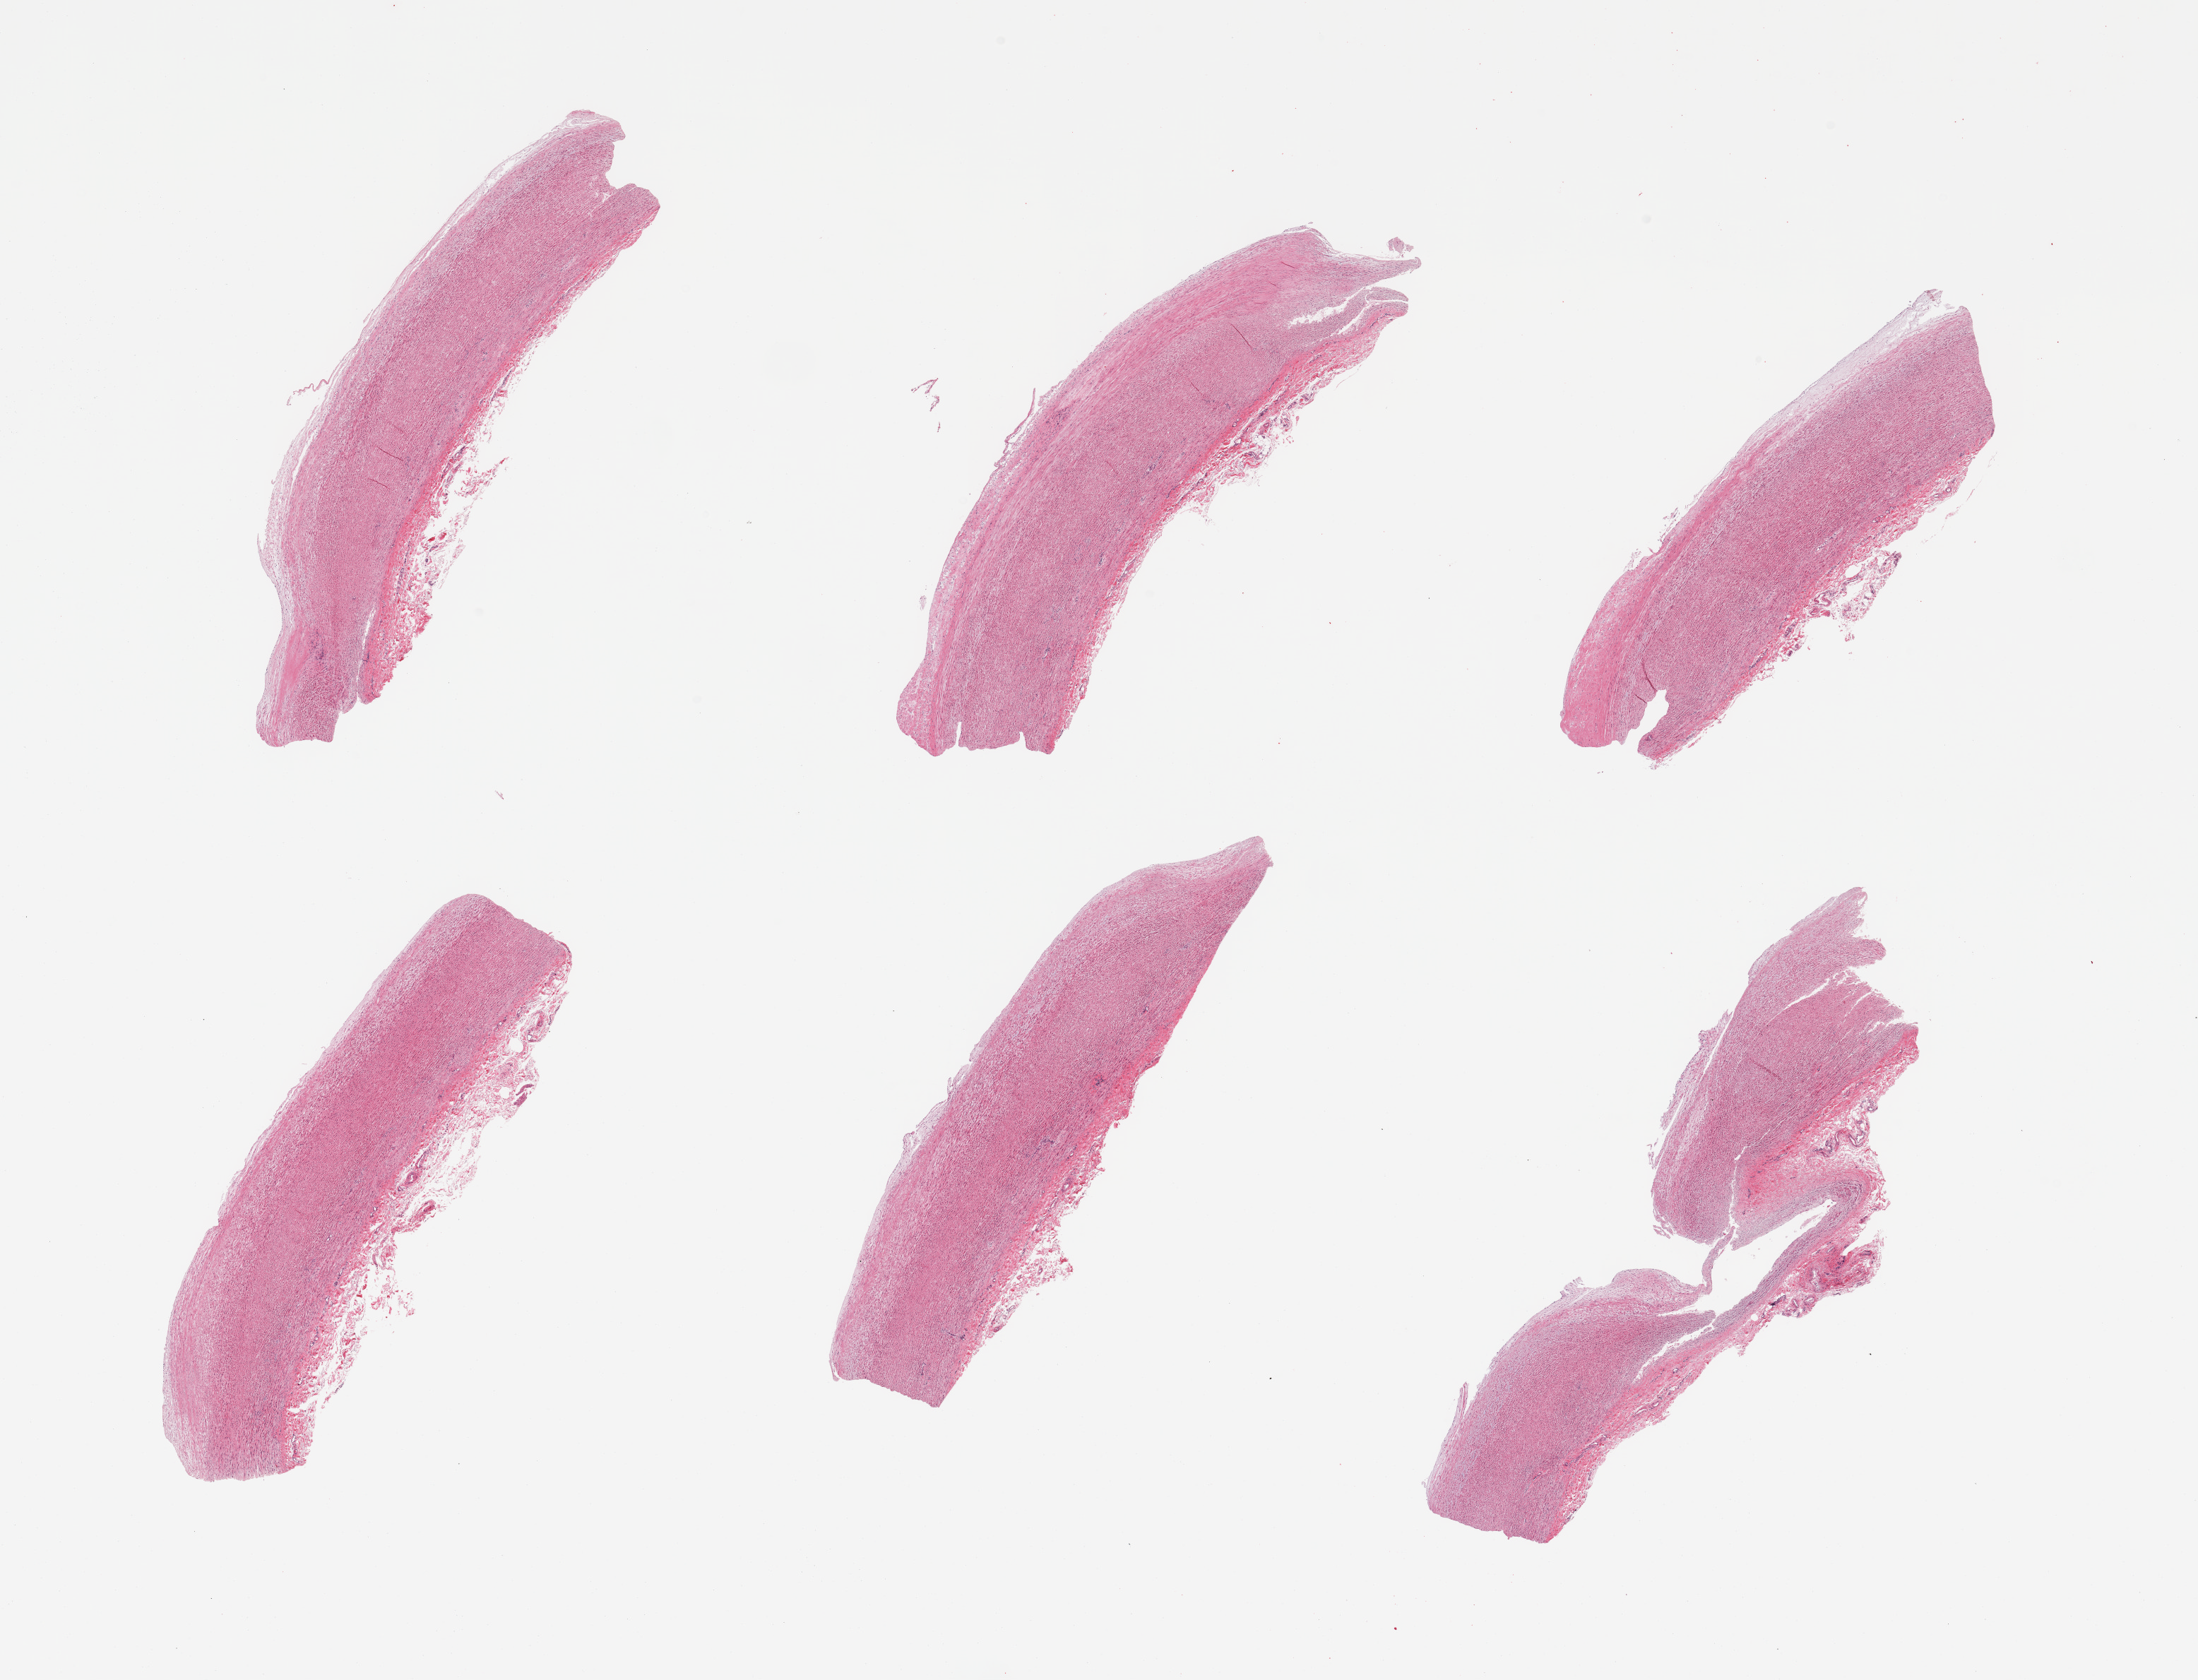
Haematoxylin and eosin whole-slide image, shown as a low-resolution overview of the whole scanned area (about 24.6 x 18.8 mm, from a 20x scan); PAXgene-fixed paraffin-embedded (PFPE) section; target tissue: aorta; donor tissue sample.
Reviewer comment on this tissue sample: 6 pieces, trace atherosis.